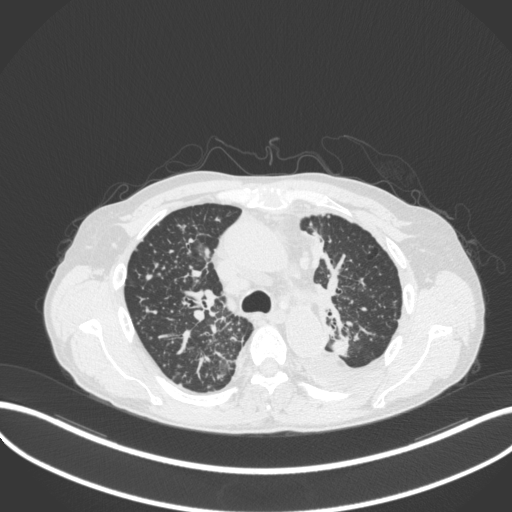
Chest CT, one axial slice; slice 249 of 319 in the series (ordered by position); 120 kVp; lung window (W 1500 / L -600 HU); 1 mm slice thickness; 512 × 512 image matrix, field of view 400 × 400 mm. Patient: male, 58 years. From the clinical record (not read from this slice): clinical TNM (as recorded): T1c N3 M1.
Outlined on this slice (bounding box drawn by a radiologist):
- lung tumour (recorded histology: adenocarcinoma): bounding box <325,332,353,361> (left, top, right, bottom; pixels)